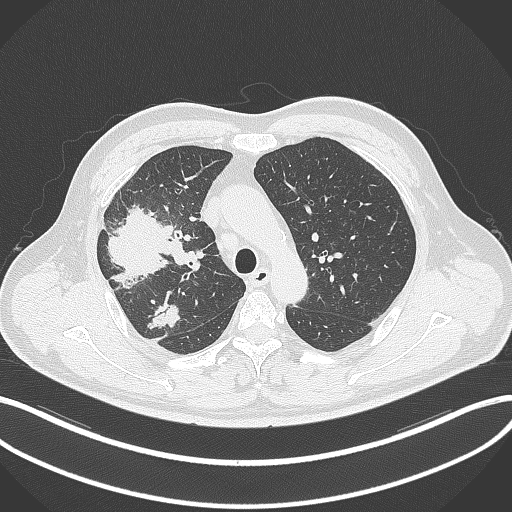
Chest CT, one axial slice; position 239 of 348 along the scan axis; reconstruction kernel B70f; 120 kVp; lung window (W 1500 / L -600 HU); 512 × 512 image matrix, field of view 400 × 400 mm. Male patient, age 55 years. Case-level facts recorded for this patient, not image findings: clinical TNM (as recorded): T3 N2 M1.
Annotated regions visible in this slice (rectangle marked by the reading radiologist):
- lung tumour (recorded histology: adenocarcinoma): bounding box [x1, y1, x2, y2] px = [103, 201, 173, 290]